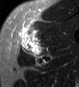
MRI of an extremity soft-tissue mass, one axial slice. Position 35 of 45 along the scan axis. STIR. MR volume resampled by the dataset authors to the PET/CT grid (not the native acquisition matrix). 3.27 mm slice thickness. 79 × 87 image matrix, field of view 77 × 85 mm. Male patient. Case-level facts recorded for this patient, not image findings: histological type: pleiomorphic leiomyosarcoma; grade: high; site of the primary tumour: left thigh.
Structures marked on this image (expert contour drawn on MRI and transferred to this co-registered scan by the dataset authors):
- gross tumour volume including surrounding oedema: bounding box <20,25,44,56> (left, top, right, bottom; pixels)